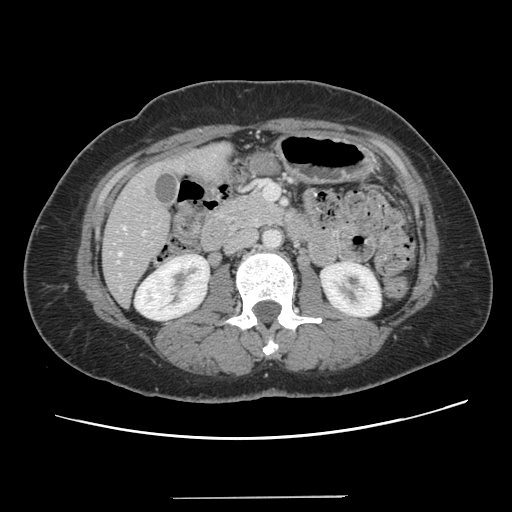
Contrast-enhanced abdominal CT, one axial slice. Position 46 of 141 along the scan axis. 120 kVp. Intravenous contrast given. Soft-tissue window (W 400 / L 40 HU). 2.5 mm slice thickness. 512 × 512 image matrix. Female patient, age 53 years. From the clinical record (not read from this slice): diagnosis: colorectal cancer liver metastases, imaged before liver resection.
Annotated regions visible in this slice (outlined manually by an expert reader):
- hepatic veins: bounding box [x1, y1, x2, y2] px = [118, 227, 125, 255]
- liver: [104, 146, 228, 304]
- planned liver remnant (the part of the liver to remain after resection): [103, 217, 170, 305]